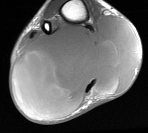
MRI of an extremity soft-tissue mass, one axial slice; position 26 of 76 along the scan axis; MR volume resampled by the dataset authors to the PET/CT grid (not the native acquisition matrix); 3.27 mm slice thickness; 148 × 133 image matrix, field of view 145 × 130 mm. Male patient. Case-level facts recorded for this patient, not image findings: histological type: liposarcoma - round cell; grade: high; site of the primary tumour: right calf.
Annotated regions visible in this slice (expert contour drawn on MRI and transferred to this co-registered scan by the dataset authors):
- gross tumour volume (mass): bounding box [x1, y1, x2, y2] px = [11, 14, 141, 116]